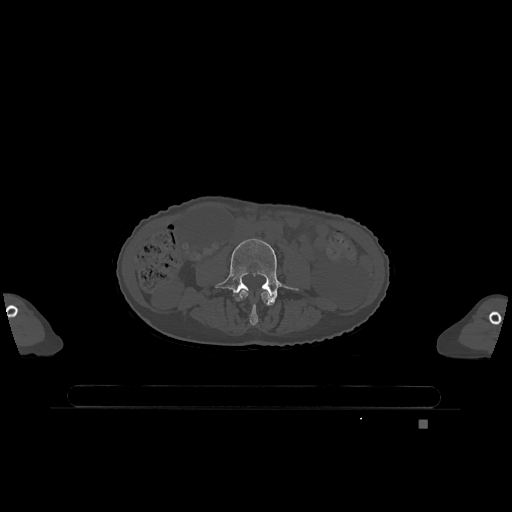
CT including the spine, one axial slice. Position 312 of 1317 along the scan axis. Bone window (W 1800 / L 400 HU). 0.5 mm slice thickness. 512 × 512 image matrix, field of view 500 × 500 mm. Patient: female, 74 years. From the clinical record (not read from this slice): primary cancer: lung.
Outlined on this slice (semi-automatically segmented with operator editing):
- L3 vertebra: box from (x=239, y=290) to (x=271, y=326) px
- L4 vertebra: (x=215, y=238)–(x=298, y=305)